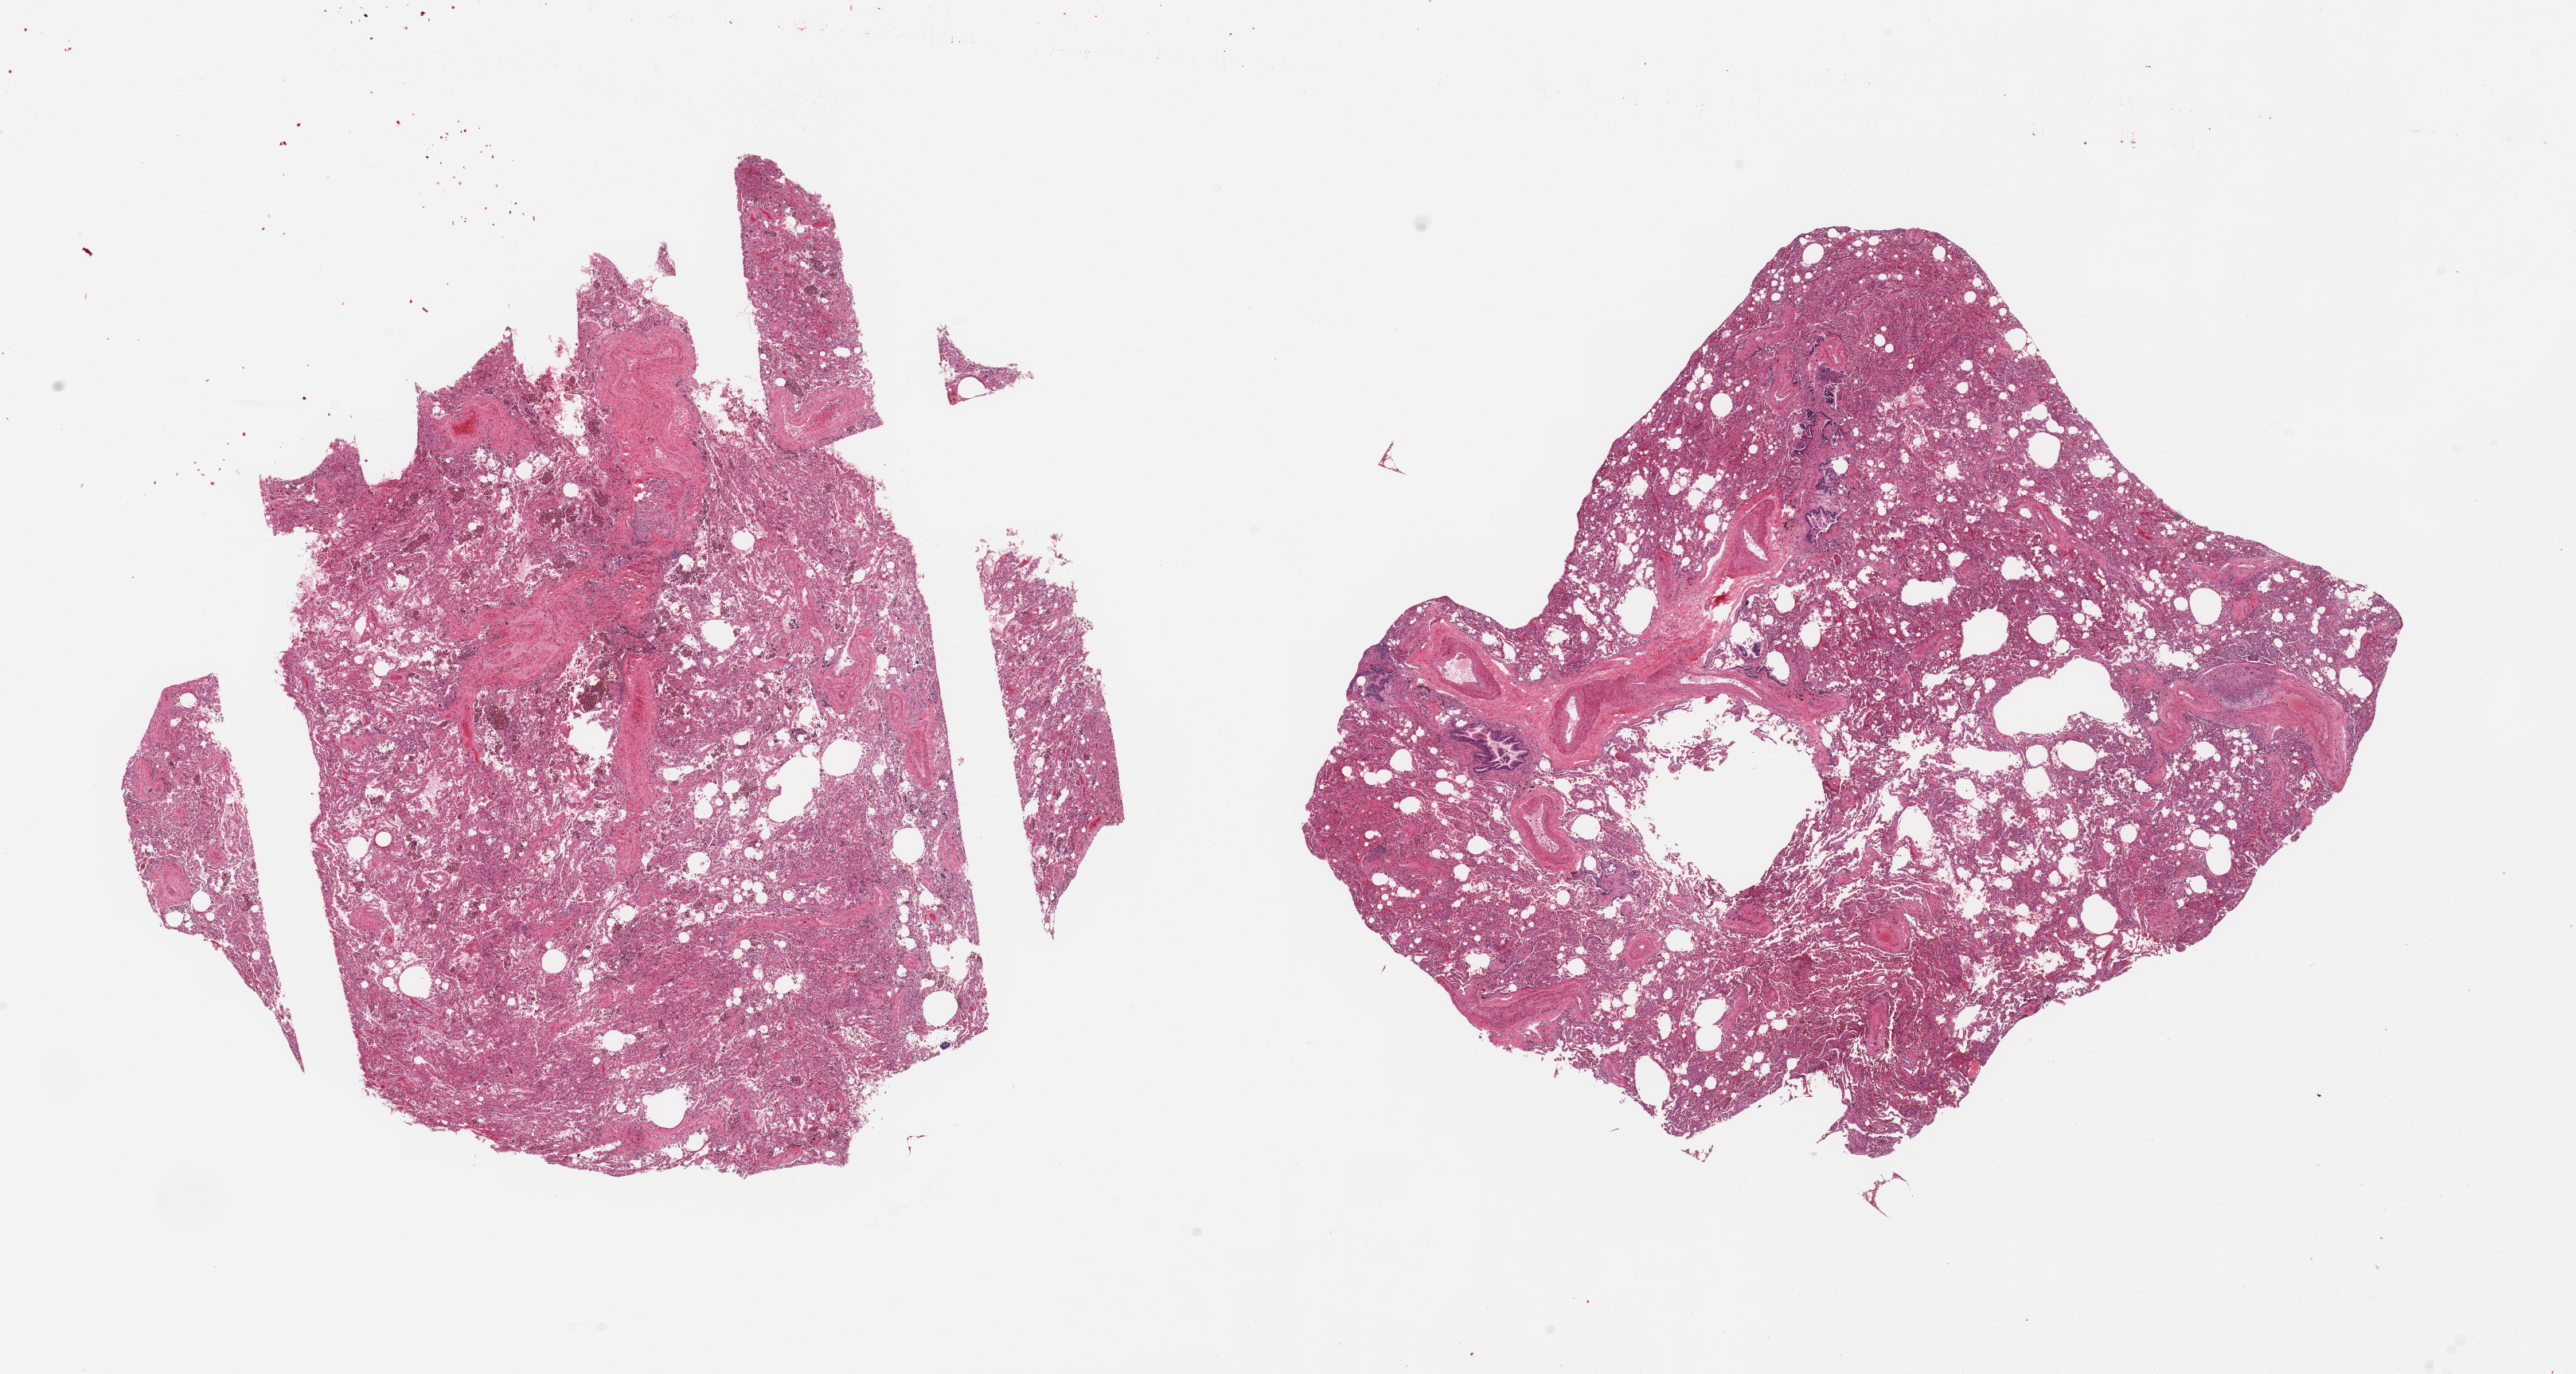
Whole-slide image, haematoxylin and eosin stain — a low-resolution overview of the entire scanned area, about 25.6 x 13.7 mm (slide scanned at 20x); PAXgene-fixed, paraffin-embedded tissue; target tissue: lung; donor tissue sample. Donor sex: male.
Review note (as recorded): 2 pieces; numerous pigmented alveolar macrophages.